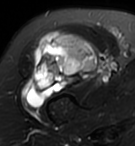
MRI of an extremity soft-tissue mass, one axial slice. Position 72 of 95 along the scan axis. T2-weighted fat-saturated. MR volume resampled by the dataset authors to the PET/CT grid (not the native acquisition matrix). 3.27 mm slice thickness. 135 × 146 image matrix, field of view 132 × 143 mm. Female patient. Case-level facts recorded for this patient, not image findings: histological type: pleiomorphic undifferentiated sarcoma; grade: high; site of the primary tumour: right quadricep.
Annotated regions visible in this slice (expert contour drawn on MRI and transferred to this co-registered scan by the dataset authors):
- gross tumour volume including surrounding oedema: box from (x=23, y=31) to (x=100, y=106) px
- gross tumour volume (mass): (x=23, y=31)–(x=100, y=106)